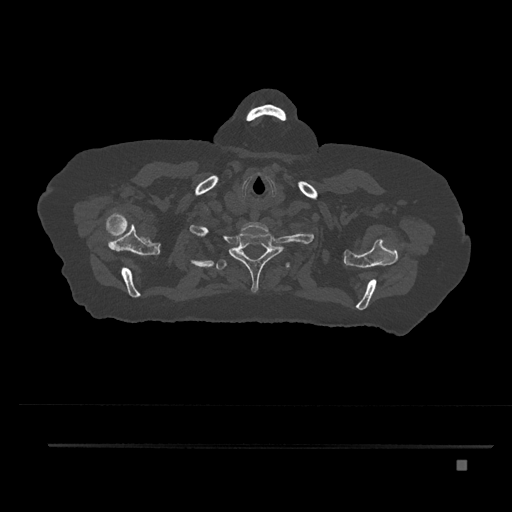
CT including the spine, one axial slice; slice 696 of 797 in the series (ordered by position); reconstruction kernel Br40s/3; bone window (W 1800 / L 400 HU); 0.5 mm slice thickness; 512 × 512 image matrix, field of view 437 × 437 mm. Female patient, age 76 years. From the clinical record (not read from this slice): primary cancer: lung; vertebrae with lytic lesions (as recorded): T11, L3.
Annotated regions visible in this slice (semi-automatic segmentation, software-assisted and operator-edited):
- T1 vertebra: bounding box <229,231,282,292> (left, top, right, bottom; pixels)
- T2 vertebra: <207,248,290,270>